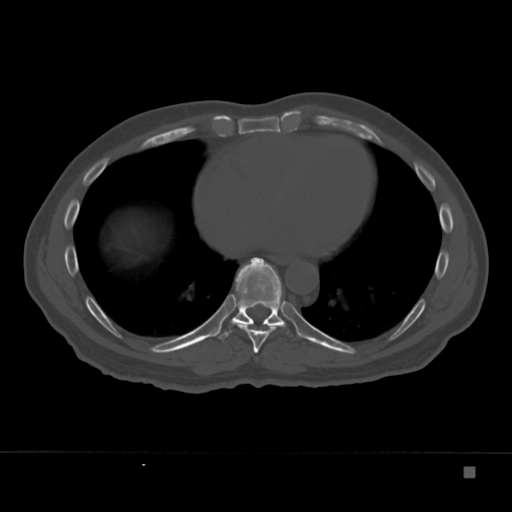
CT including the spine, one axial slice; slice 198 of 332 in the series (ordered by position); reconstruction kernel Br40s; 120 kVp; bone window (W 1800 / L 400 HU); 512 × 512 image matrix, field of view 389 × 389 mm. Patient: male, 72 years. Case-level facts recorded for this patient, not image findings: primary cancer: skeletal.
Structures marked on this image (semi-automatic segmentation, software-assisted and operator-edited):
- T8 vertebra: box from (x=239, y=325) to (x=277, y=353) px
- T9 vertebra: (x=213, y=257)–(x=301, y=339)